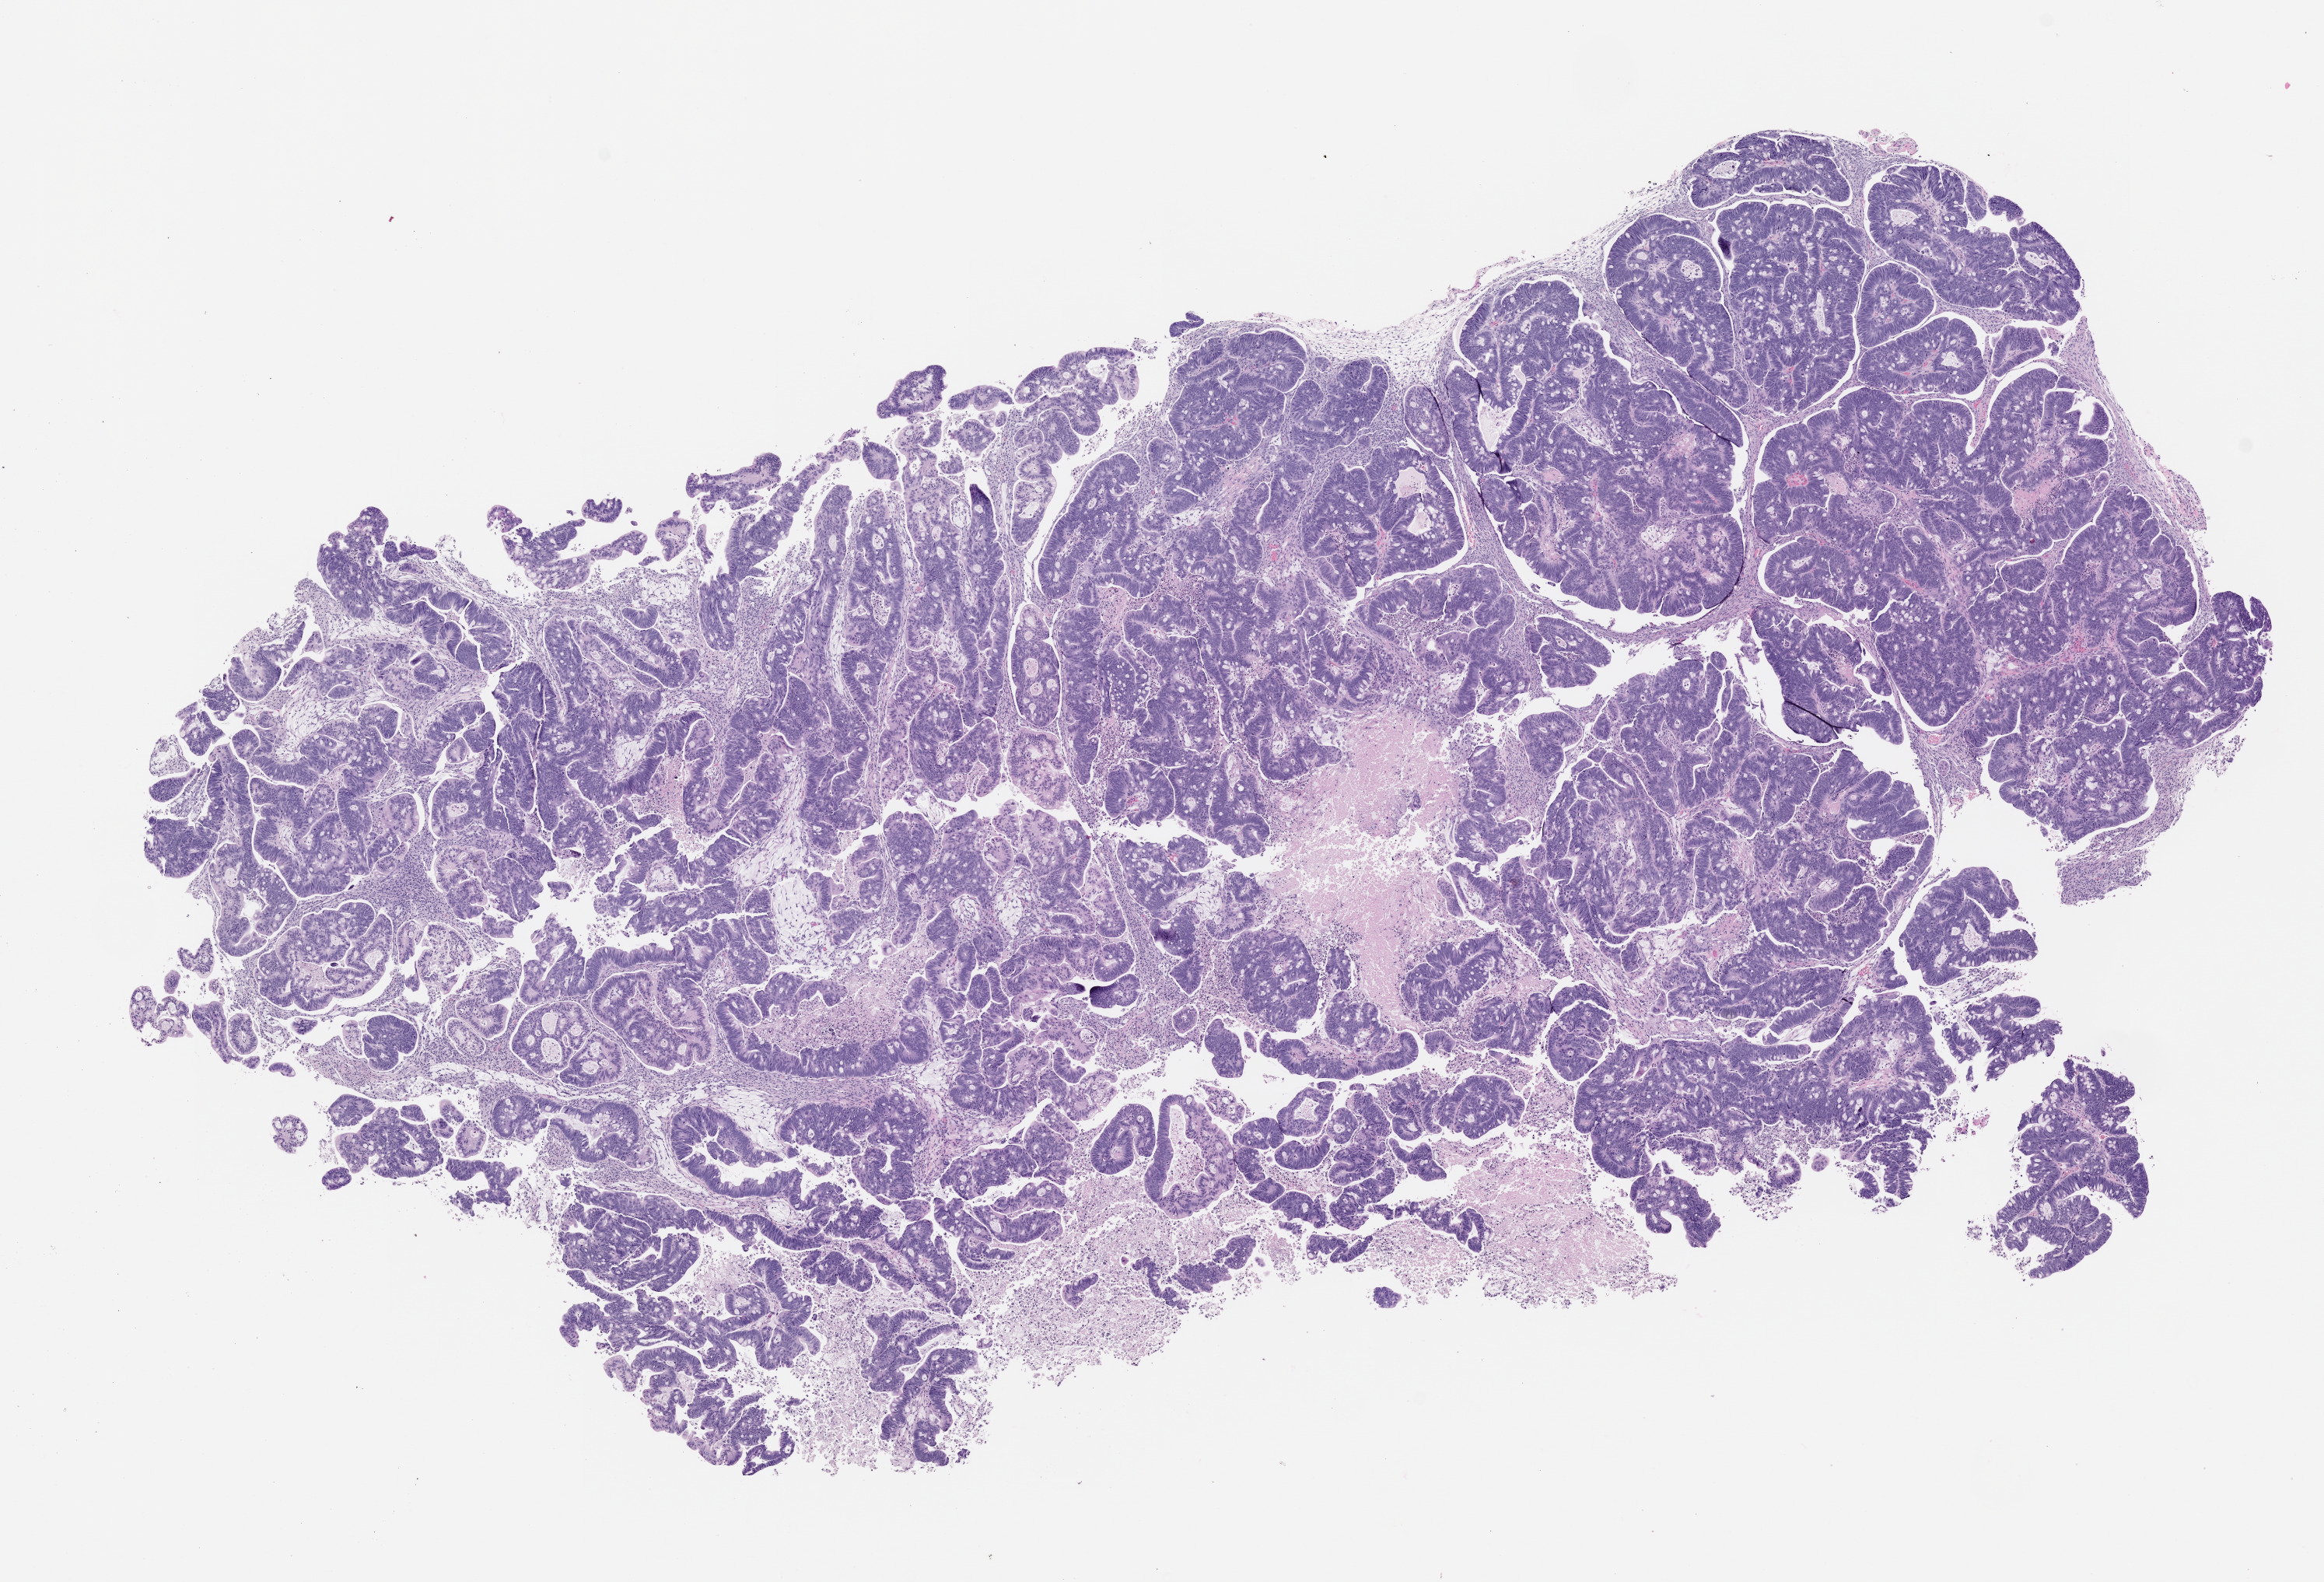
H&E whole-slide image of a patient-derived xenograft (PDX) tumor grown in a mouse, passage 2 — shown as a low-resolution overview of the whole scanned area (about 12.0 x 8.2 mm). Formalin-fixed paraffin-embedded section. Tumor site category: colon.
Originating patient diagnosis: Colon Adenocarcinoma.